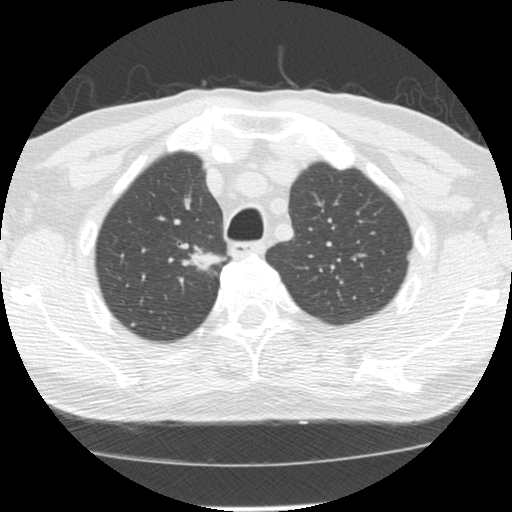
Chest CT (low-dose screening protocol), one axial image; first (baseline) screen; lung window (W 1500 / L -600 HU); 2.5 mm slice thickness; standard (soft-tissue) reconstruction kernel (STANDARD); 120 kVp; slice 32 of 139 in the series; 512 × 512 image matrix, field of view 310 × 310 mm. Male, age 64 years at enrolment. Former smoker at enrolment.
Lesion marked by an expert reader, box from (x=173, y=235) to (x=223, y=277) px. Reader record for this screening exam (exam-level; its link to the box is not recorded): non-calcified nodule or mass ≥4 mm, right upper lobe, 20 × 13 mm, spiculated (stellate) margins, soft tissue attenuation.